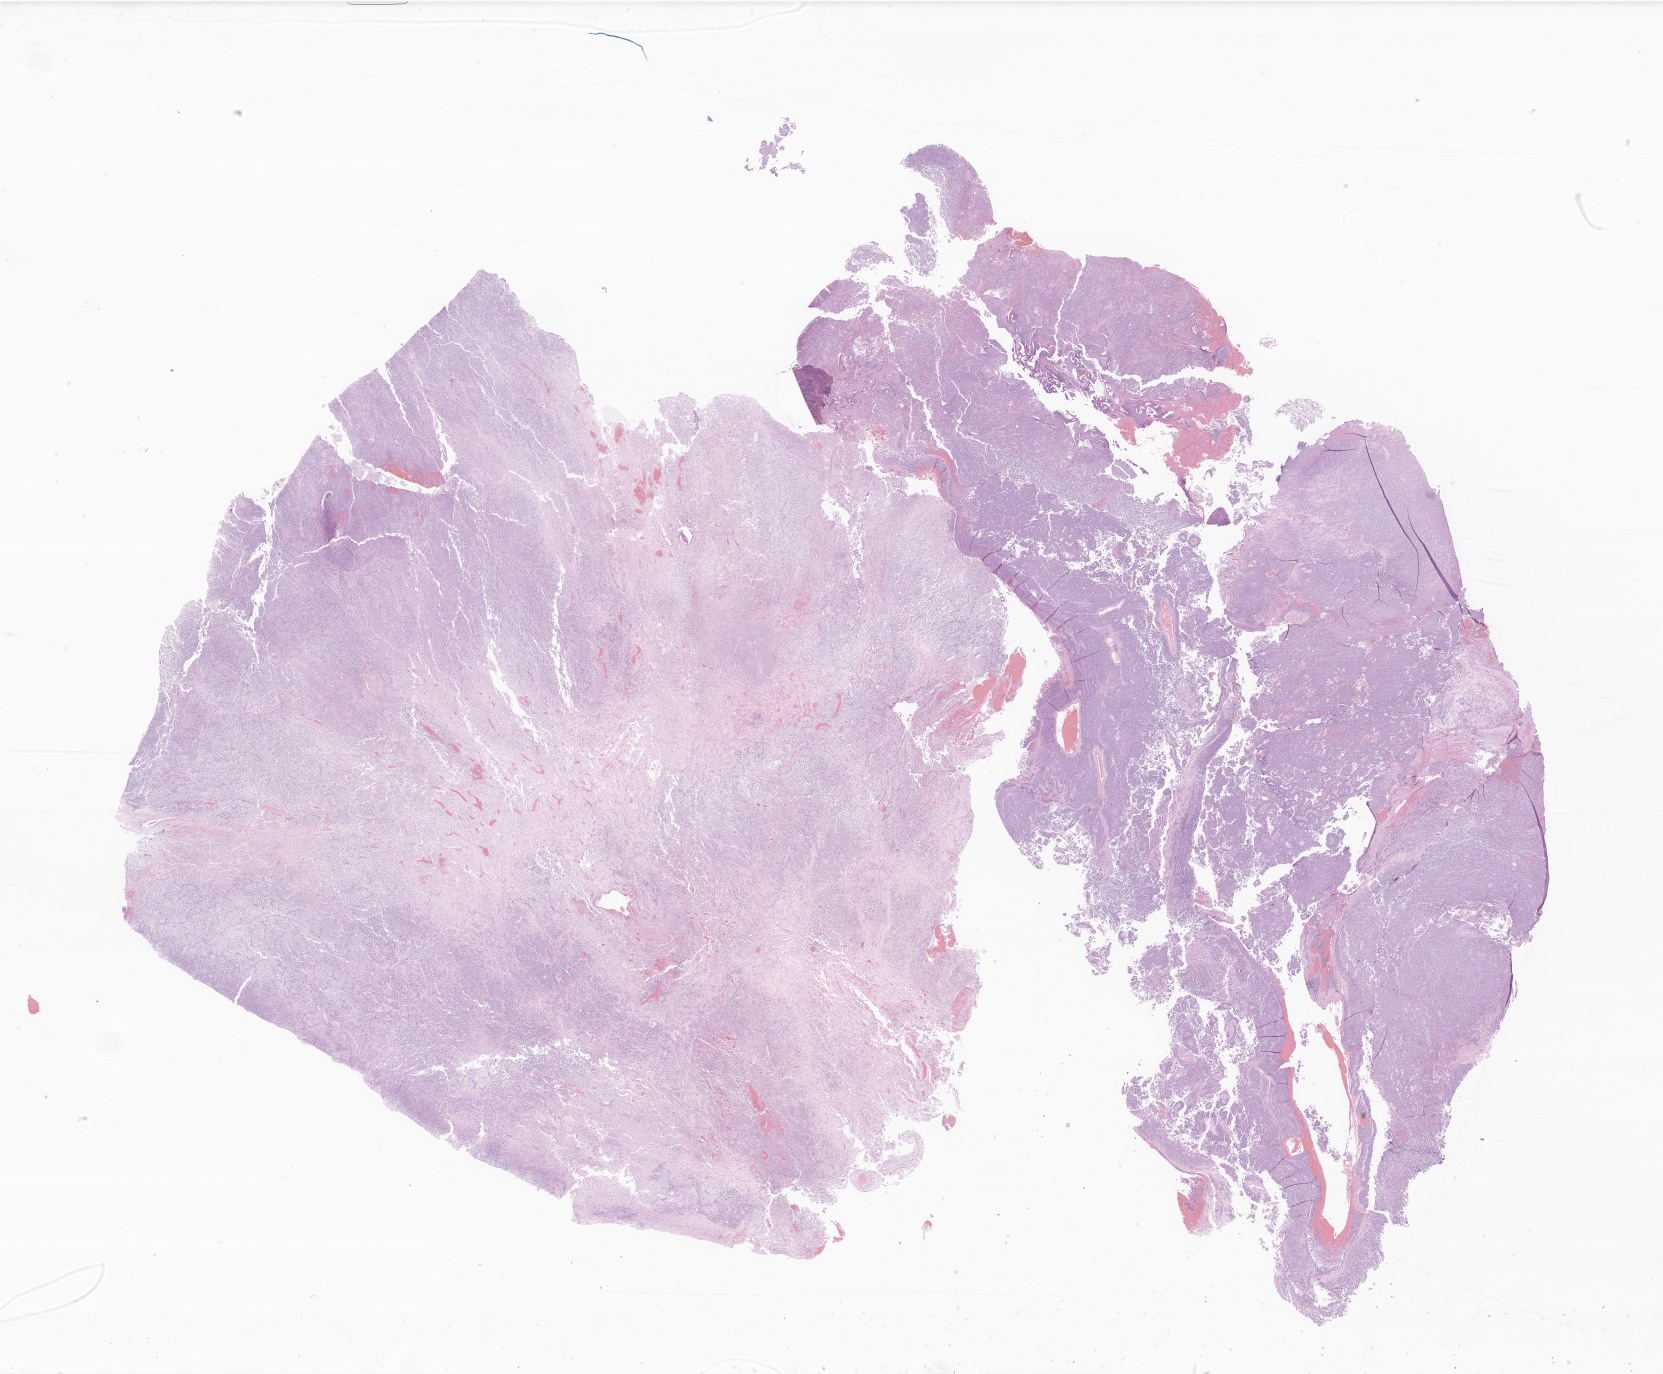
Hematoxylin and eosin (H&E) whole-slide image of tumor tissue from the frontal lobe — low-resolution overview of the scanned area, about 28.1 x 23.2 mm, FFPE section. Patient female; age 39 months (3 years 3 months).
Recorded diagnosis: CNS embryonal tumor, NOS.